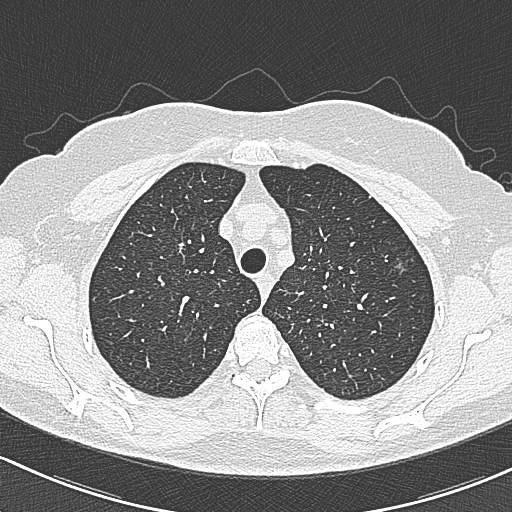
Axial slice from a low-dose chest CT screening exam, baseline annual screen, lung window (W 1500 / L -600 HU), lung (sharp) reconstruction kernel (B80f), 120 kVp, slice 65 of 312 in the series, 512 × 512 image matrix. Female participant, aged 65 years at enrolment. Current smoker at enrolment.
Expert-annotated lung lesion, bounding box (x1, y1, x2, y2) in pixels: (385, 257, 420, 287). The screening reader recorded 3 non-calcified nodules or masses ≥4 mm on this exam (left upper lobe, left upper lobe, right upper lobe); which of them this box marks is not recorded. Official screen result: positive, change unspecified: nodule(s) >= 4 mm or enlarging nodule(s), mass(es), or other non-specific abnormalities suspicious for lung cancer. Later outcome: lung cancer diagnosed 390 days after this screen — bronchiolo-alveolar carcinoma, non-mucinous, left upper lobe, stage IA (AJCC 6th edition), 10 mm at pathology.